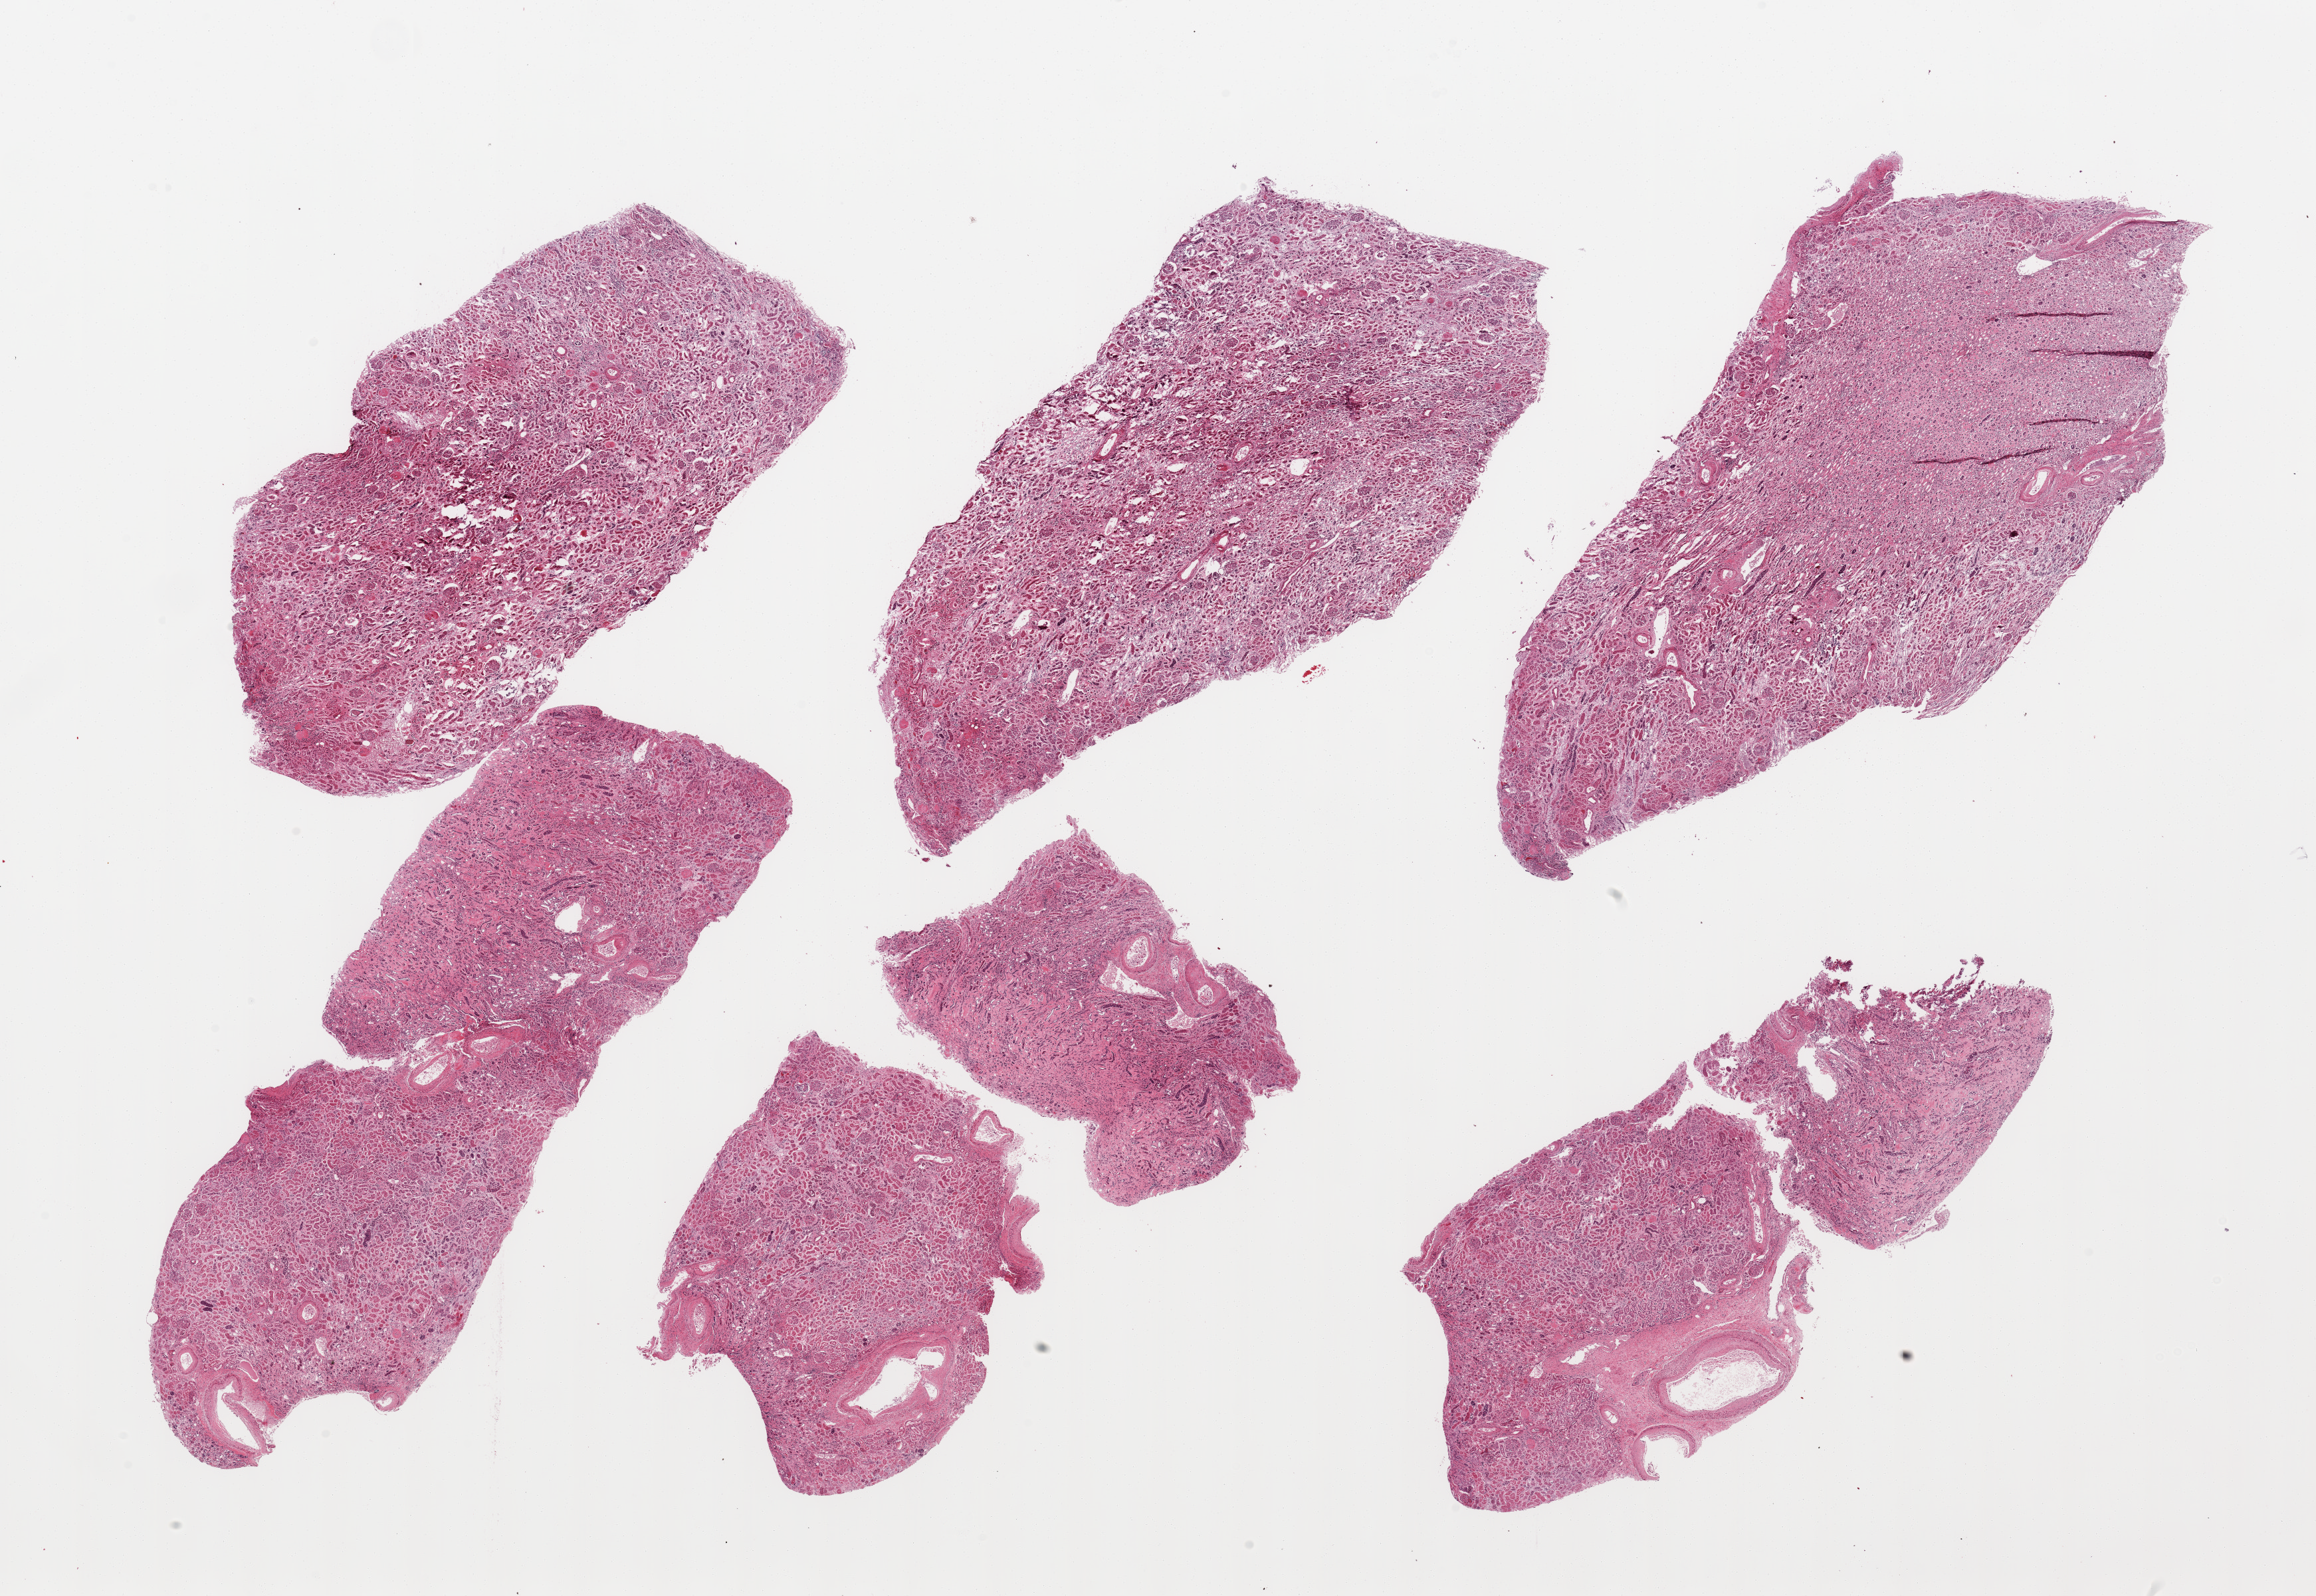
Digitized haematoxylin and eosin-stained section — shown as a low-resolution overview of the whole scanned area (about 27.6 x 19.0 mm); PAXgene-fixed, paraffin-embedded tissue; sampled site (target tissue): renal cortex; tissue donor sample.
Reviewer comment on this tissue sample: 6 pieces (fragmented): glomeruli present, advanced tubular autolysis.